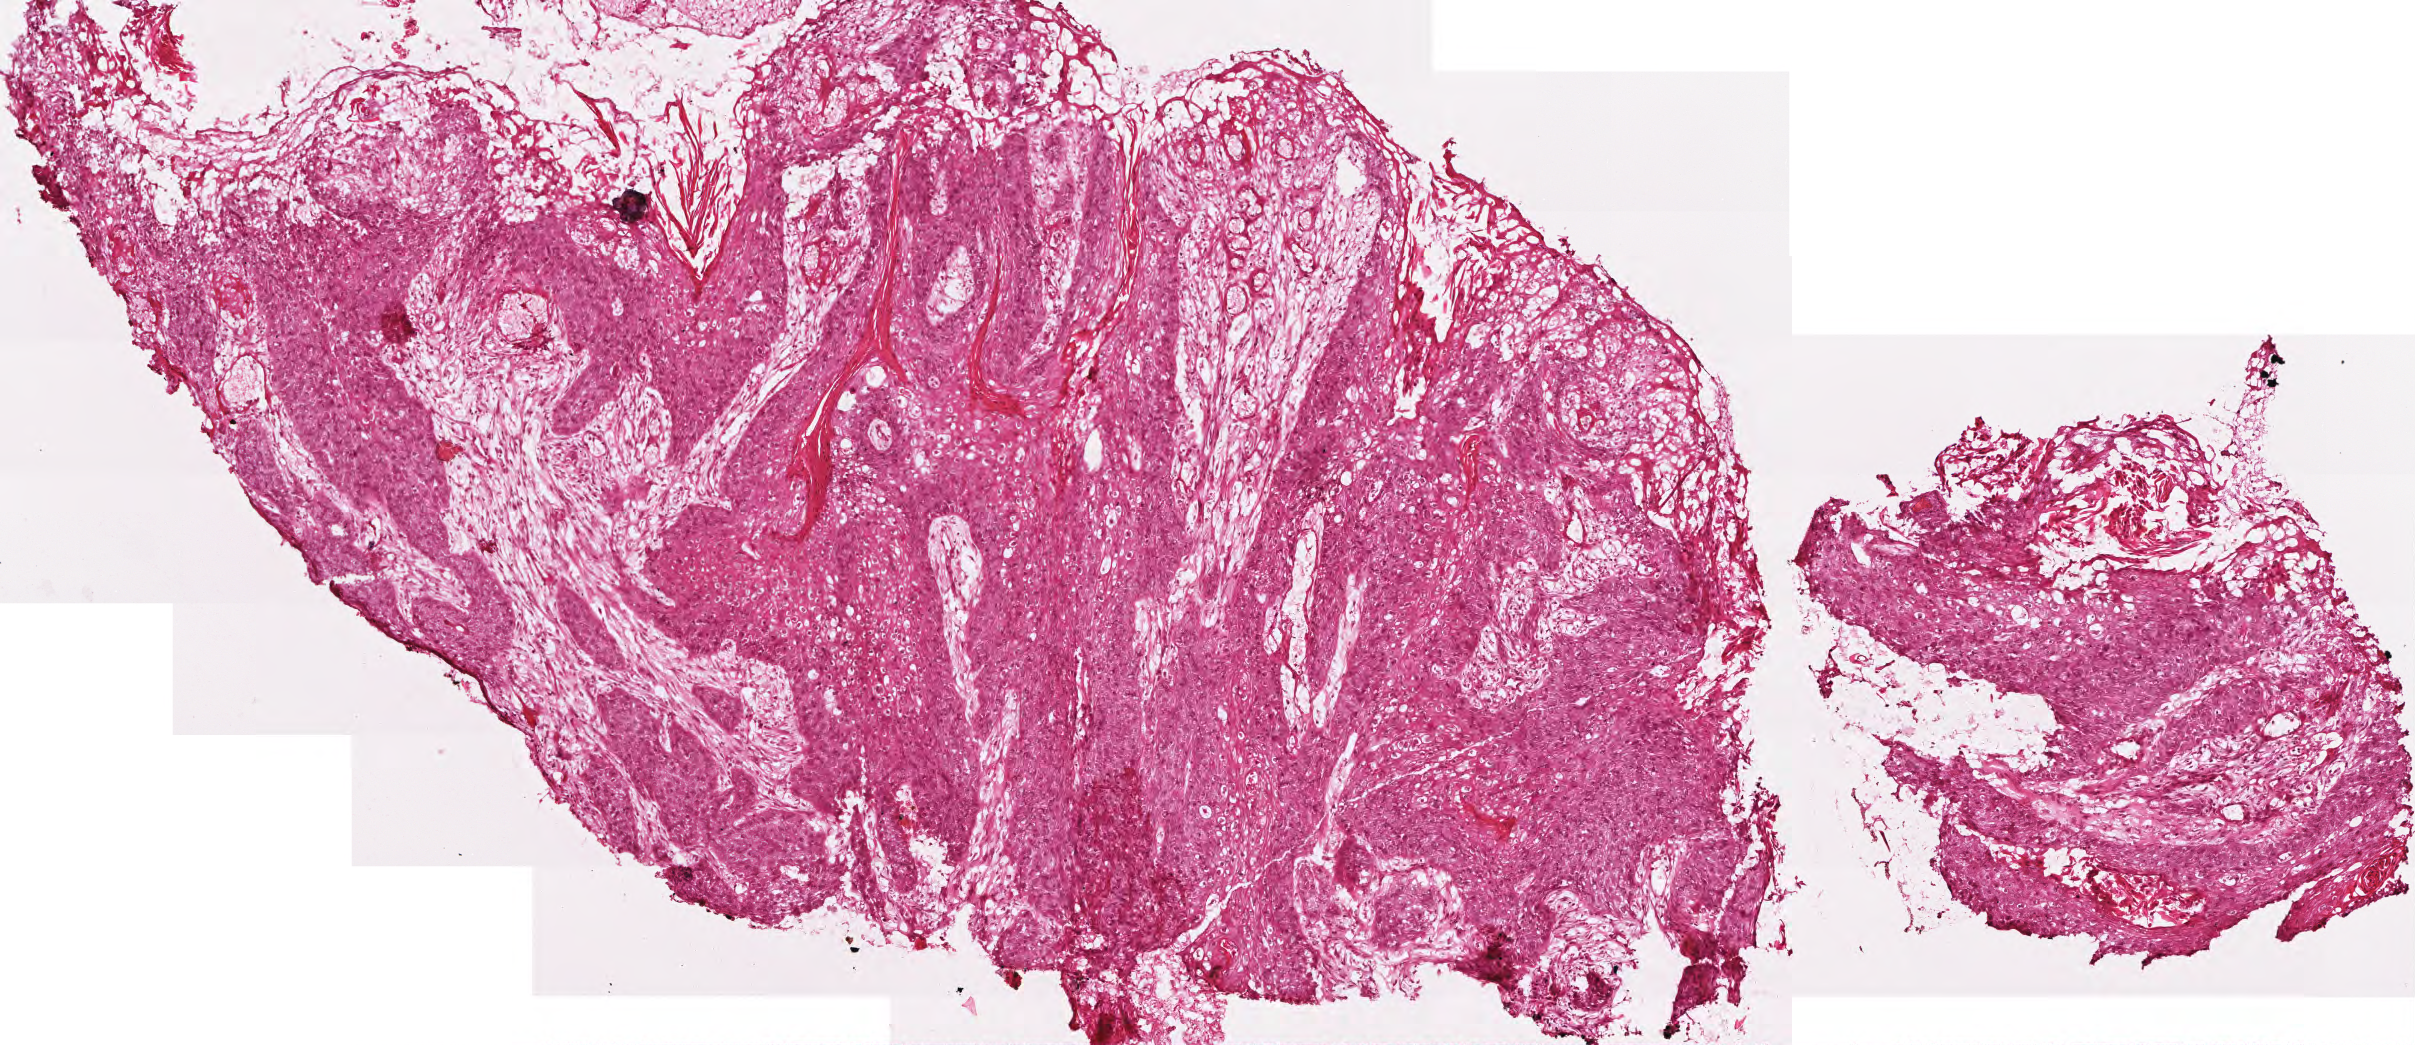
Digitized Hematoxylin and eosin (H&E) stained tissue section (whole slide), low-resolution overview of the scanned area, about 4.8 x 2.1 mm, frozen section, head and neck, primary tumour sample. Male patient; age at initial diagnosis 67 years. Histologic grade: G2 (moderately differentiated). Pathologist review of this section (percent, as recorded): tumour cells 88%, tumour nuclei 80%, normal cells 0%, stromal cells 12%, necrosis 0%. Infiltration values recorded for this section: lymphocyte infiltration 5%, monocyte infiltration 0%, neutrophil infiltration 0%.
Laterality: right. AJCC pathologic stage: IVA. Diagnosis: Squamous cell carcinoma, NOS.